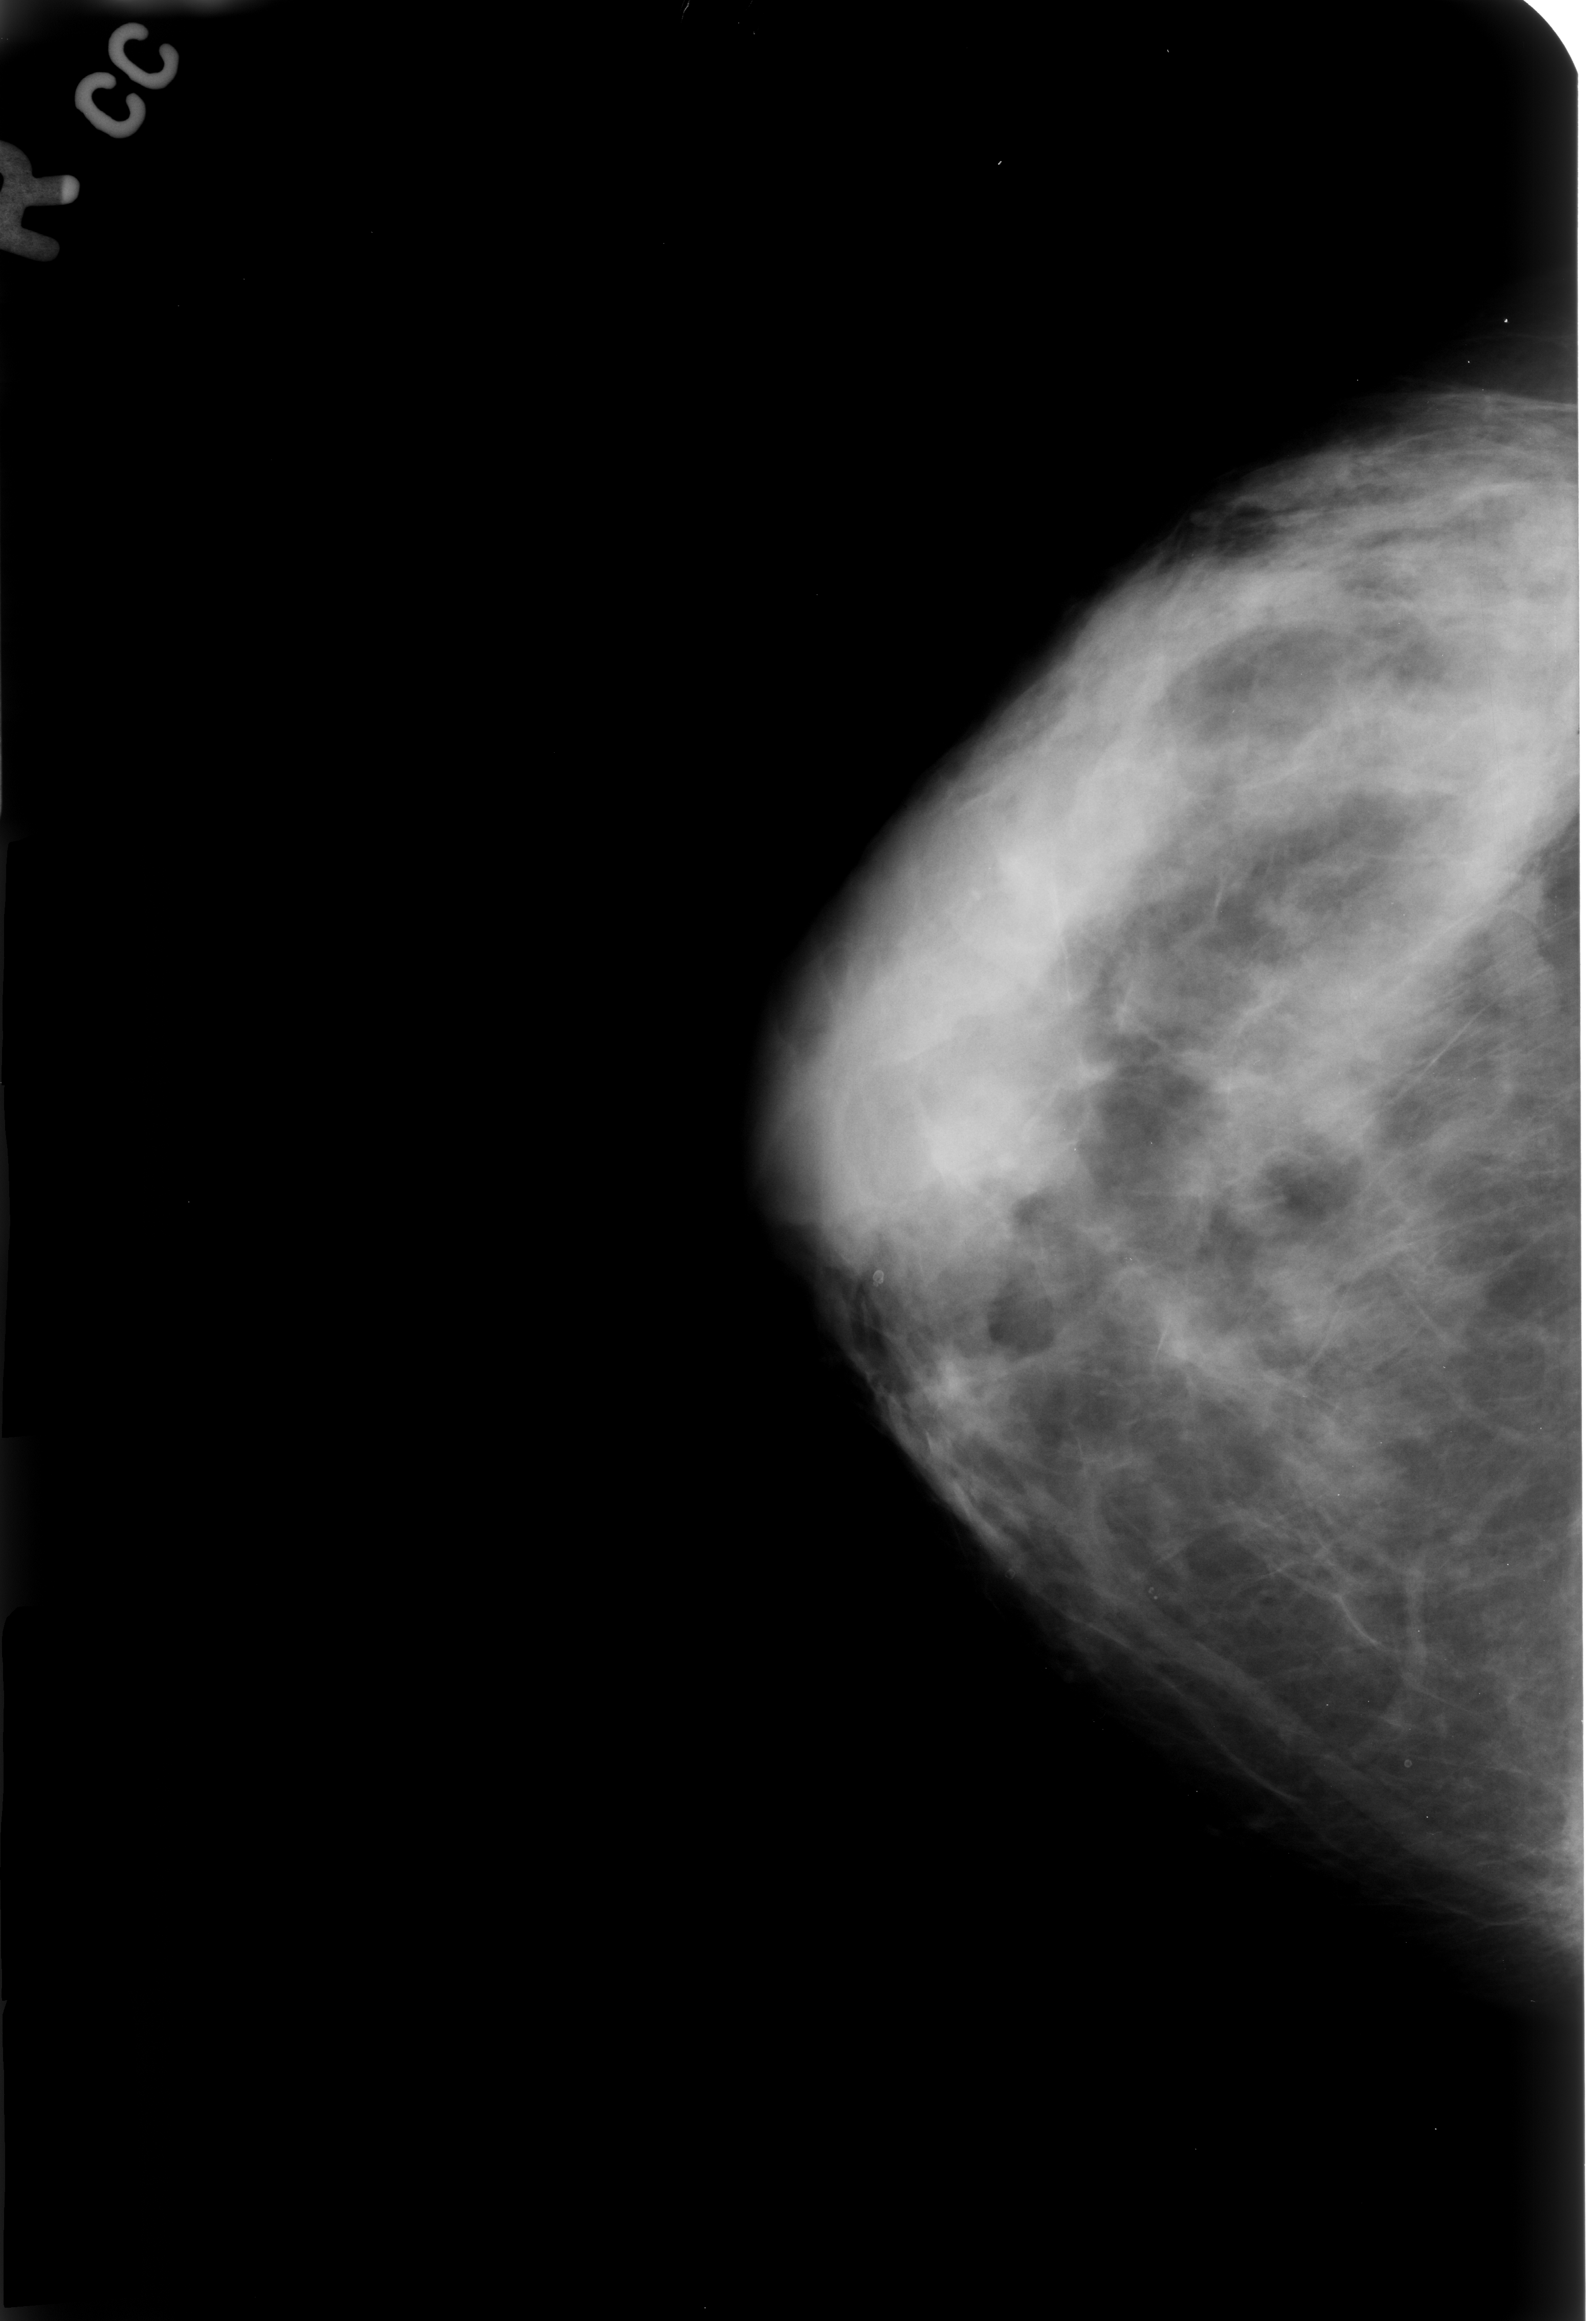
Mammogram (digitized film). Right breast. CC view. 1596 × 2321 image matrix.
Expert-marked regions of interest on this image (one box per marked abnormality):
- calcifications, morphology lucent center; BI-RADS assessment category 2; benign; no additional work-up was recommended (outcome (as recorded, no biopsy): benign without callback): bounding box <1088,1338,1139,1364> (left, top, right, bottom; pixels)